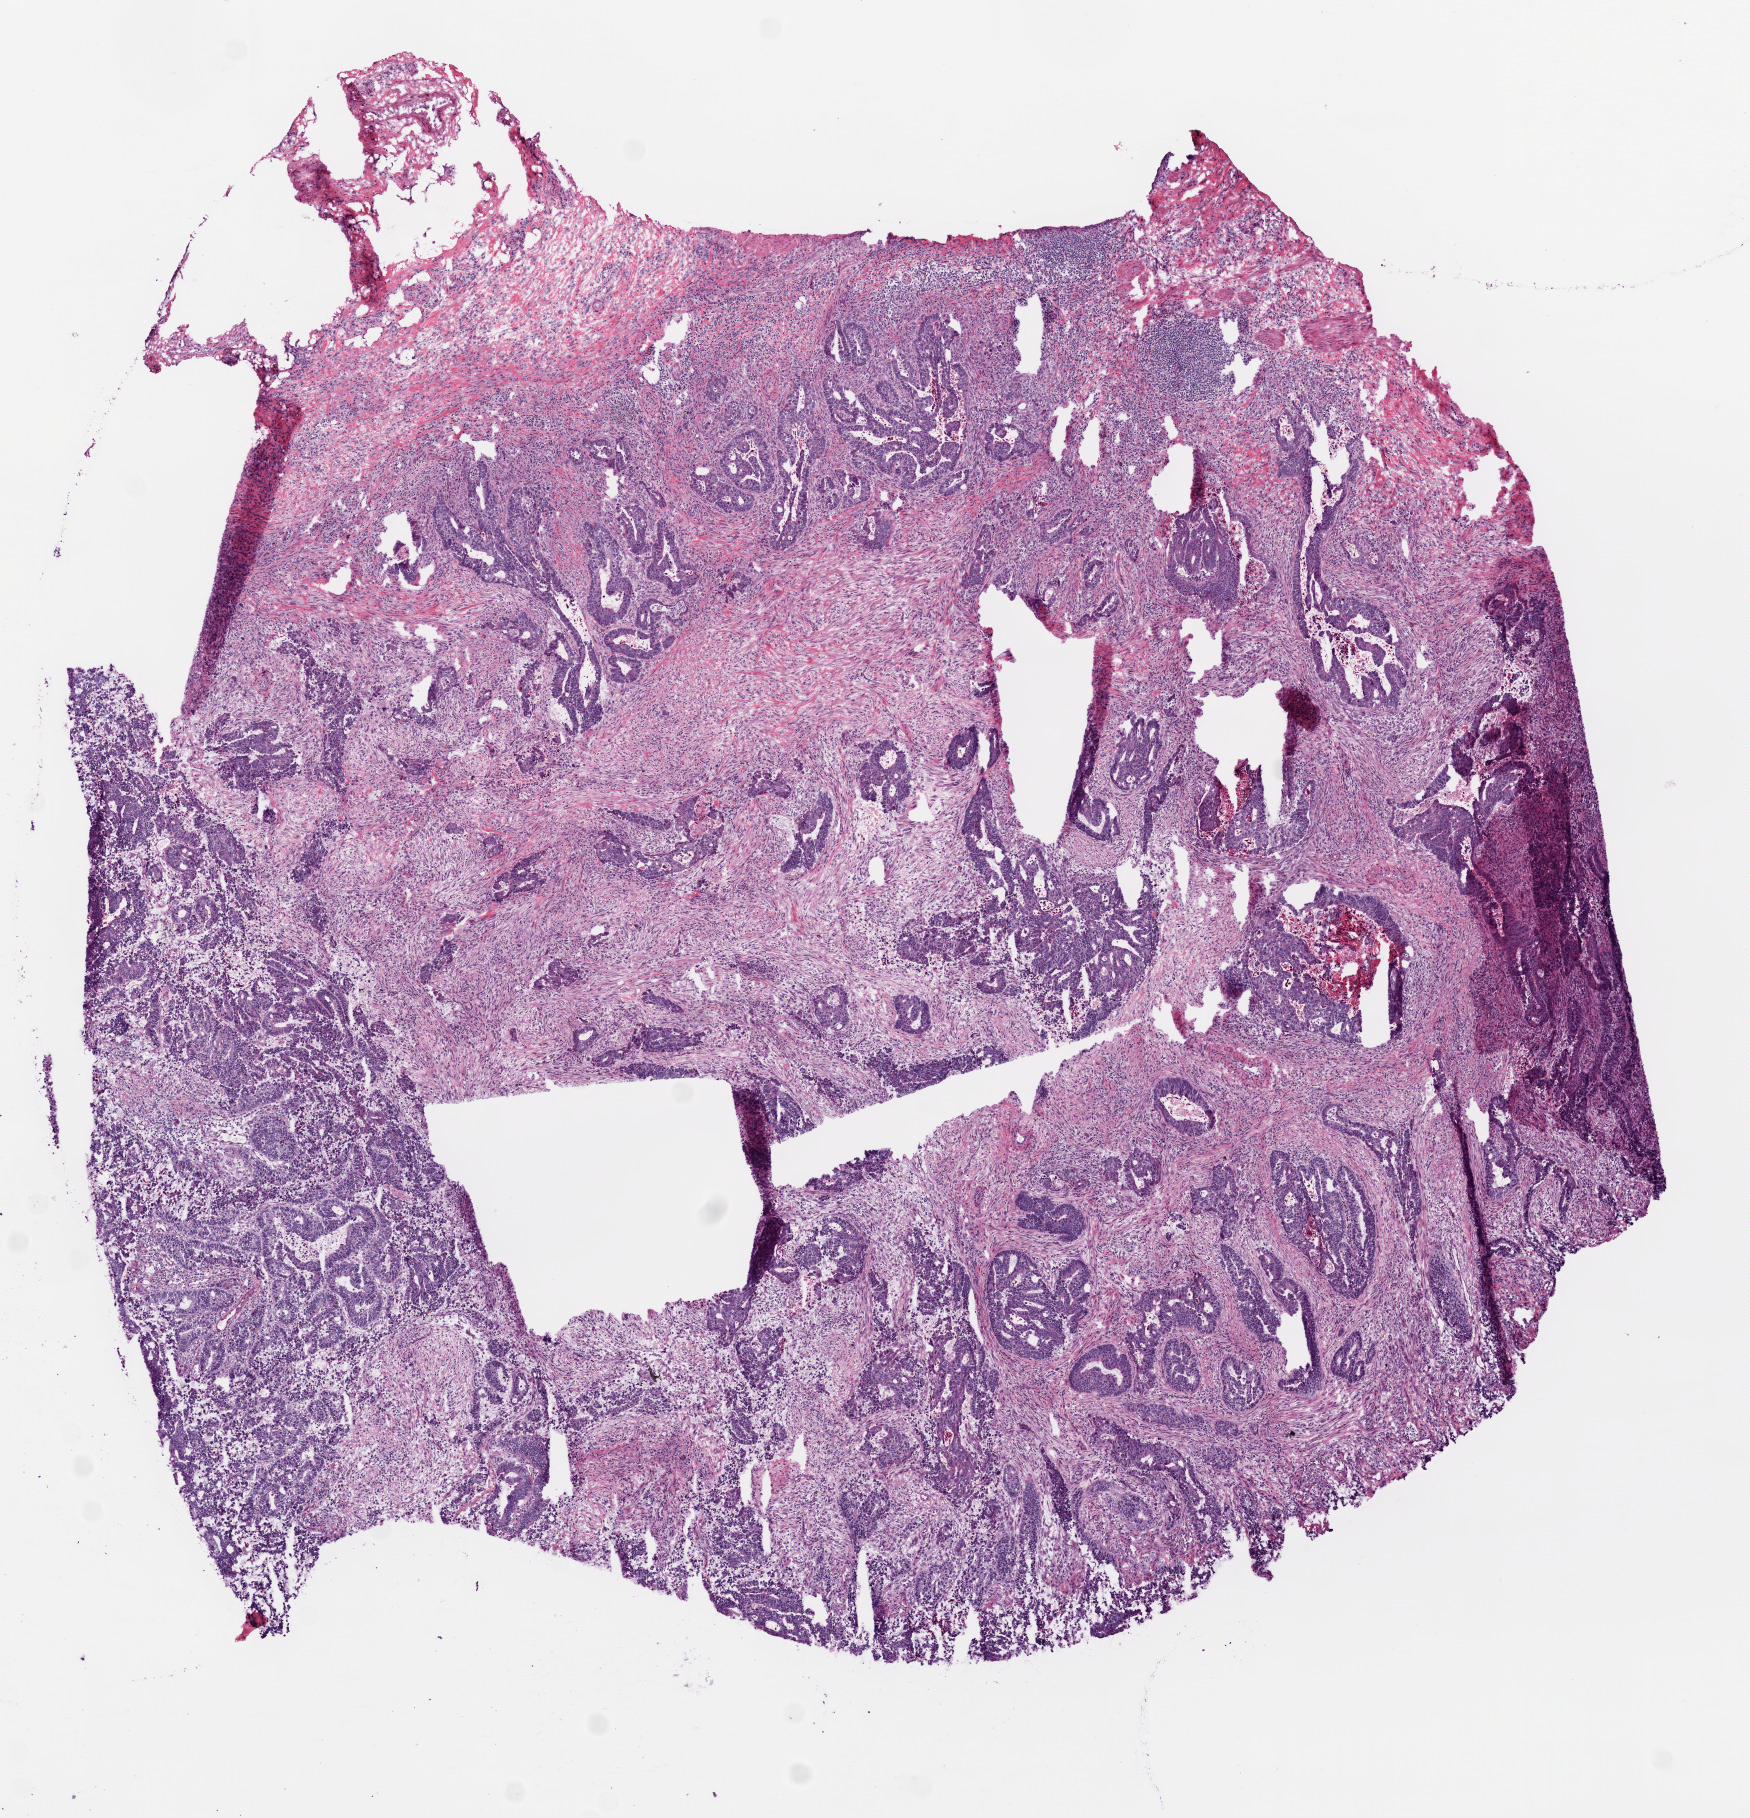
Whole-slide histology image, H&E — shown as a low-resolution overview of the whole scanned area (about 7.0 x 7.3 mm); frozen section from the bottom of the tissue portion; sample: primary tumour, rectum. Male, age 83 years at initial diagnosis. Composition of this section per pathologist review: tumour cells 67%, tumour nuclei 70%, normal cells 0%, stromal cells 30%, necrosis 3%.
AJCC pathologic stage: I. Lymph nodes positive (case pathology): 0 of 16 examined. Diagnosis: Adenocarcinoma, NOS.